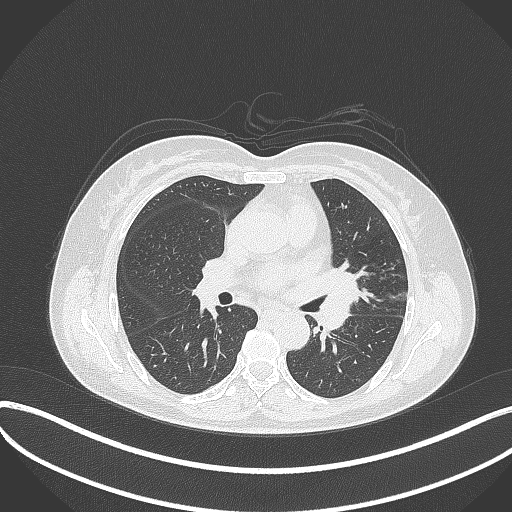
Chest CT, one axial slice. Position 192 of 373 along the scan axis. Reconstruction kernel B70f. 120 kVp. Lung window (W 1500 / L -600 HU). 1 mm slice thickness. 512 × 512 image matrix, field of view 400 × 400 mm. Female patient, age 54 years. Case-level facts recorded for this patient, not image findings: clinical TNM (as recorded): T2a N1 M0; histopathological grade: G3.
Outlined on this slice (rectangle marked by the reading radiologist):
- lung tumour (recorded histology: small cell carcinoma): bounding box <309,257,362,331> (left, top, right, bottom; pixels)